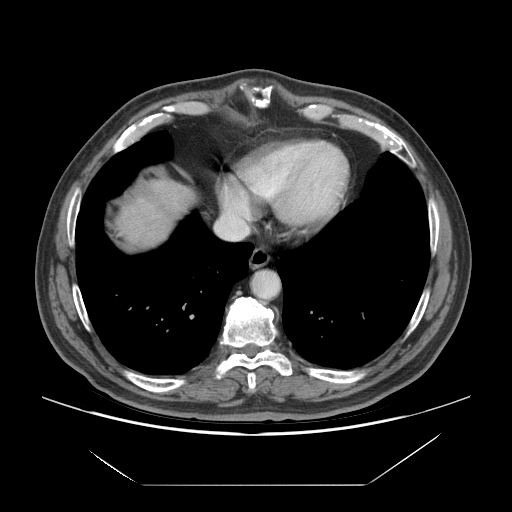
Contrast-enhanced abdominal CT (liver protocol), one axial slice; slice 67 of 75 in the series (ordered by position); reconstruction kernel STANDARD; 140 kVp; soft-tissue window (W 400 / L 40 HU); 512 × 512 image matrix. Case-level facts recorded for this patient, not image findings: diagnosis: hepatocellular carcinoma (patient treated with transarterial chemoembolisation; whether this scan precedes or follows treatment is not stated here); TNM stage (as recorded): Stage-I; Child-Pugh class: A; tumour size: 5.8 cm.
Annotated regions visible in this slice (semi-automatic segmentation, software-assisted and operator-edited):
- liver parenchyma outside the tumour (the mass and vessels are separate outlines, so this box may not span the whole liver): box from (x=118, y=180) to (x=192, y=246) px